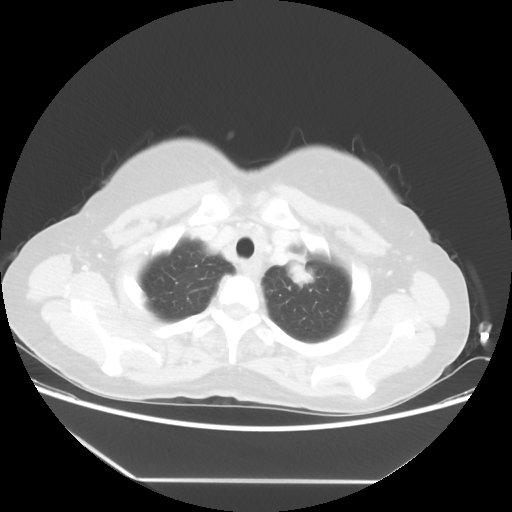
Chest CT, one axial slice. Position 46 of 52 along the scan axis. Reconstruction kernel STANDARD. Lung window (W 1500 / L -600 HU). 5 mm slice thickness. 512 × 512 image matrix. Female patient, age 50 years. Case-level facts recorded for this patient, not image findings: clinical TNM (as recorded): T2 N3 M0.
Outlined on this slice (rectangle marked by the reading radiologist):
- lung tumour (recorded histology: adenocarcinoma): bounding box <277,248,320,302> (left, top, right, bottom; pixels)